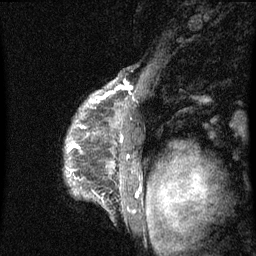
Breast MRI (dynamic contrast-enhanced), one sagittal slice. Position 52 of 60 along the scan axis. Dynamic contrast-enhanced series, image 2 of 3 at this slice position (ordered by acquisition). 1.5 T. TE 4.2 ms, TR 8 ms. 256 × 256 image matrix, field of view 190 × 190 mm. Patient: female, 50 years.
Outlined on this slice (semi-automatic segmentation, software-assisted and operator-edited):
- analysis volume of interest (the breast-tissue region the enhancement analysis was run in; not a lesion): bounding box [x1, y1, x2, y2] px = [65, 91, 142, 212]
- tumour enhancement mask (voxels above the 70 % enhancement threshold inside the analysis volume of interest): [70, 98, 122, 148]